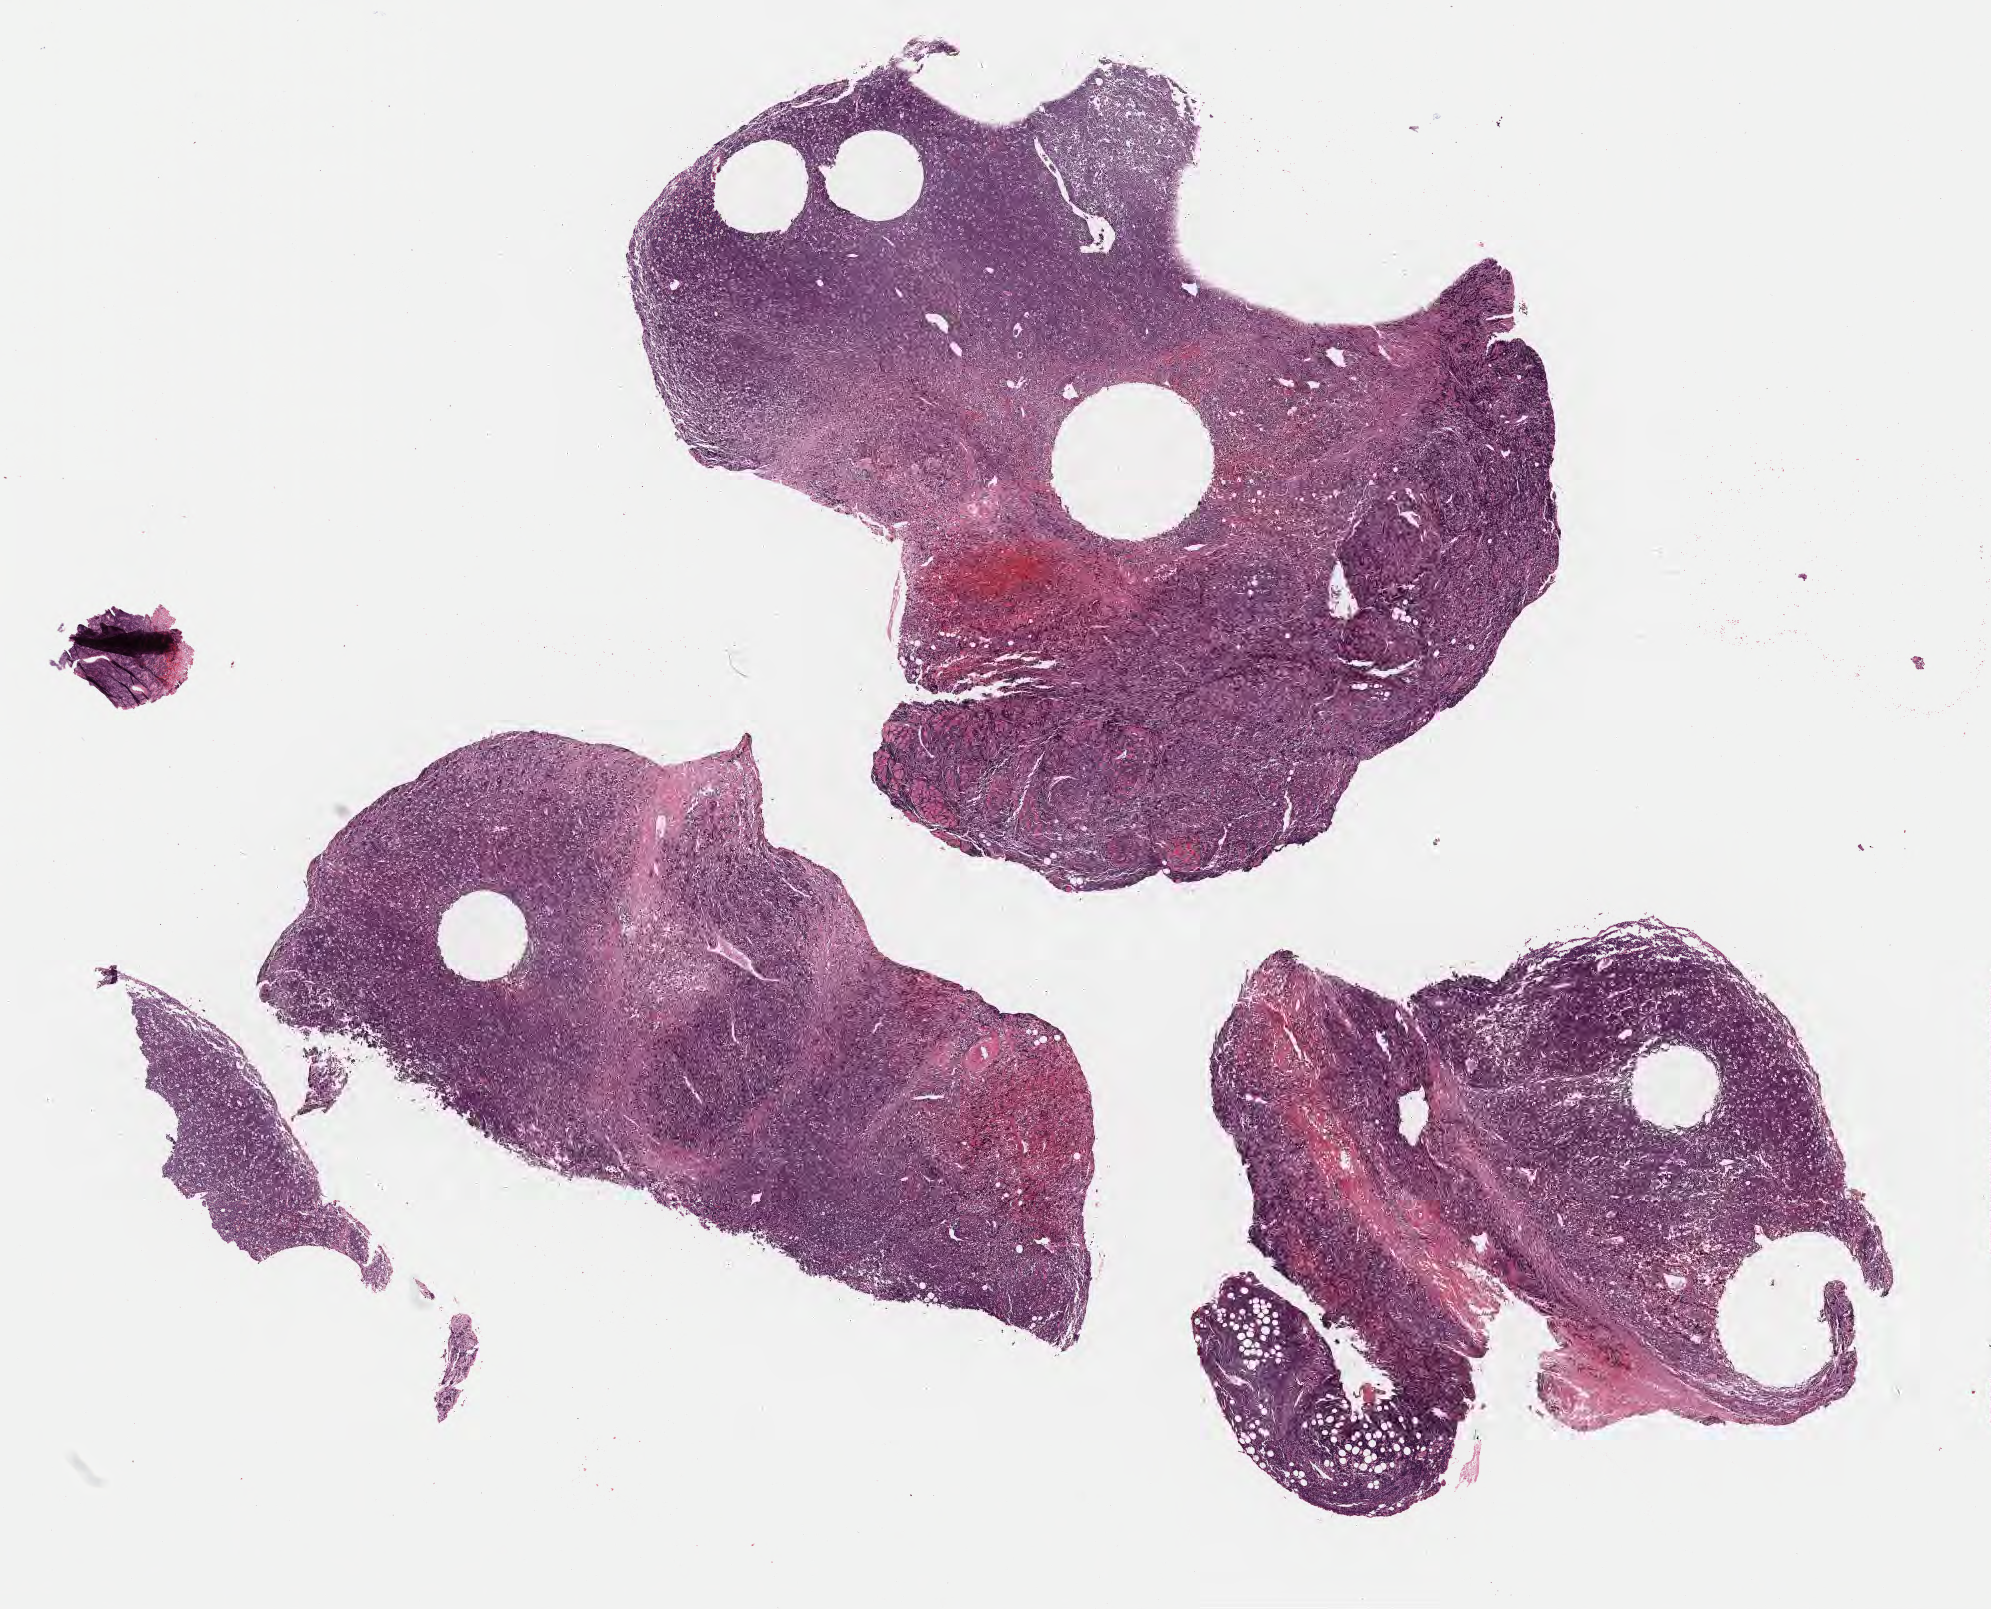
H&E whole-slide image, low-resolution overview of the scanned area, about 16.1 x 13.0 mm. FFPE section. Primary tumor. Patient male; age 15 years. Slide review estimates, as recorded: tumor cells 80%, tumor nuclei 85%, stromal cells 10%, necrosis 10%, normal cells 0%. Inflammatory infiltration, as recorded: lymphocyte infiltration 60%, monocyte infiltration 25%, neutrophil infiltration 5%.
- diagnosis: Burkitt lymphoma, NOS
- section: top of the tissue portion
- Ann Arbor stage (patient): Stage IV